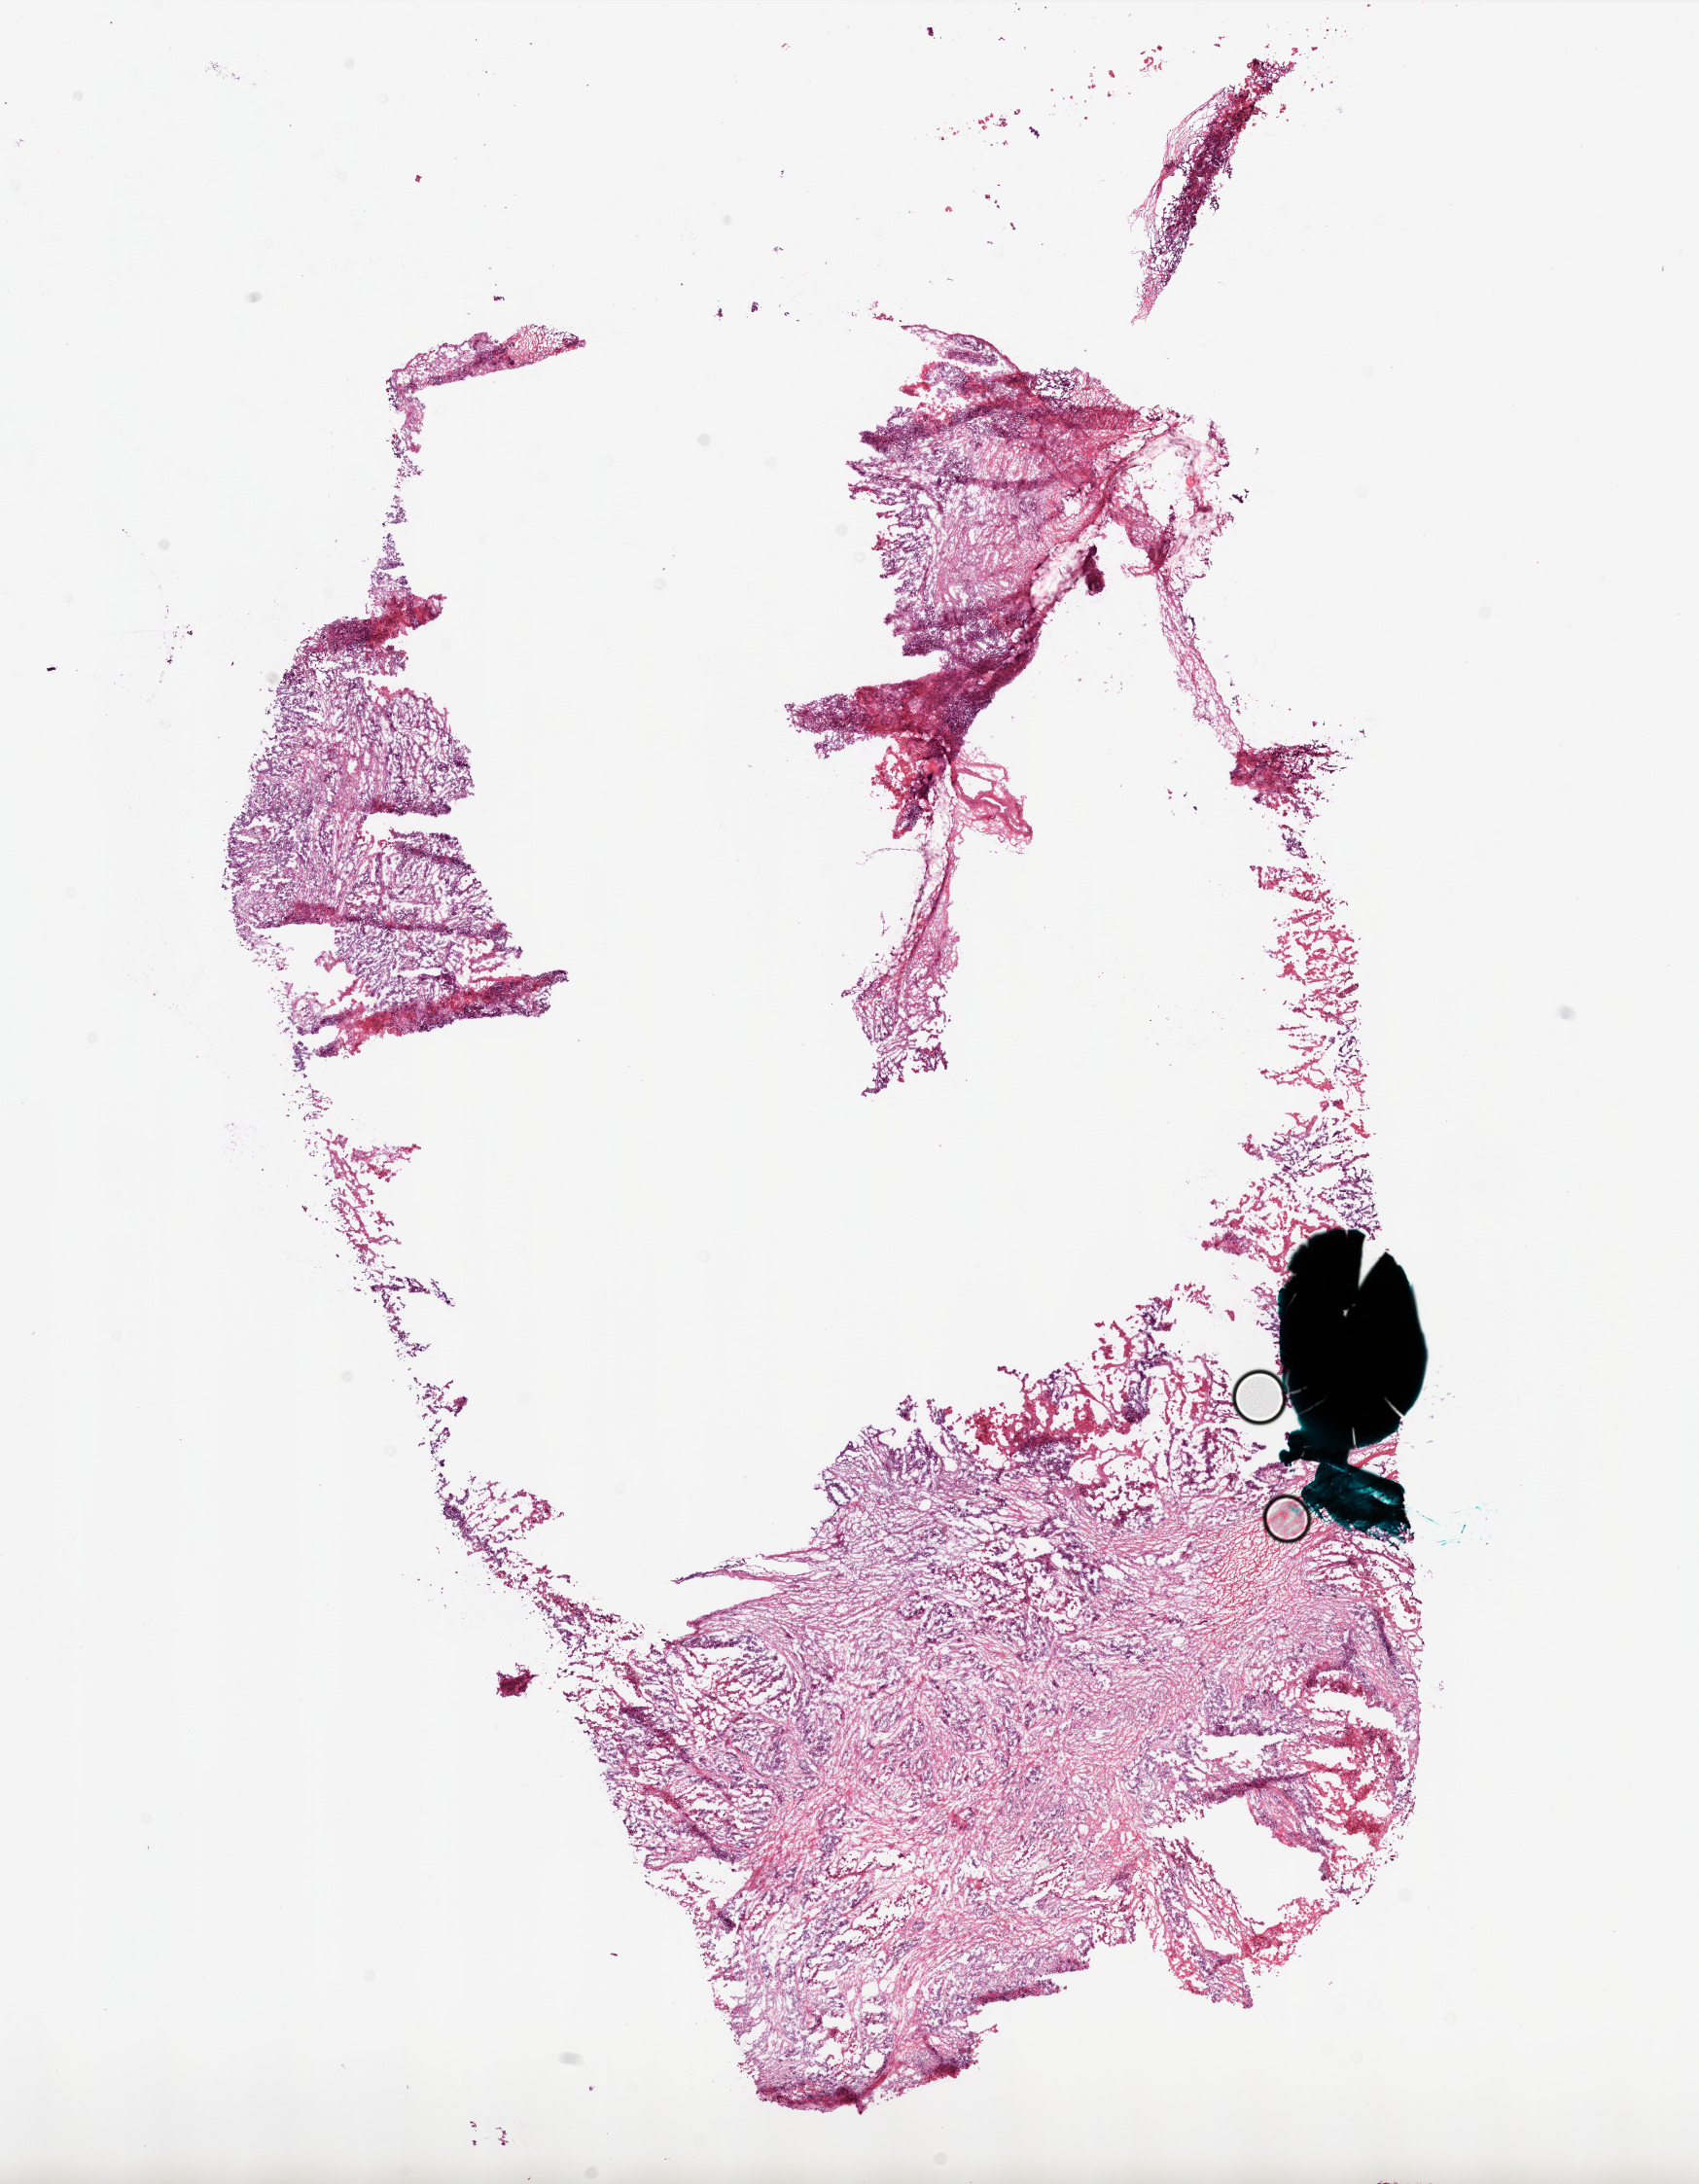
Digitized H&E tissue section (whole slide), low-resolution overview of the scanned area, about 14.0 x 18.0 mm. Frozen section. Ovary, primary tumour sample. Patient: female, age at initial diagnosis 54 years. Histologic grade: G3 (poorly differentiated). Pathologist review of this section (percent, as recorded): tumour cells 70%, tumour nuclei 80%, normal cells 0%, stromal cells 20%, necrosis 10%. Infiltration values recorded for this section: lymphocyte infiltration 100%.
• FIGO stage: IIIC
• diagnosis: Serous cystadenocarcinoma, NOS